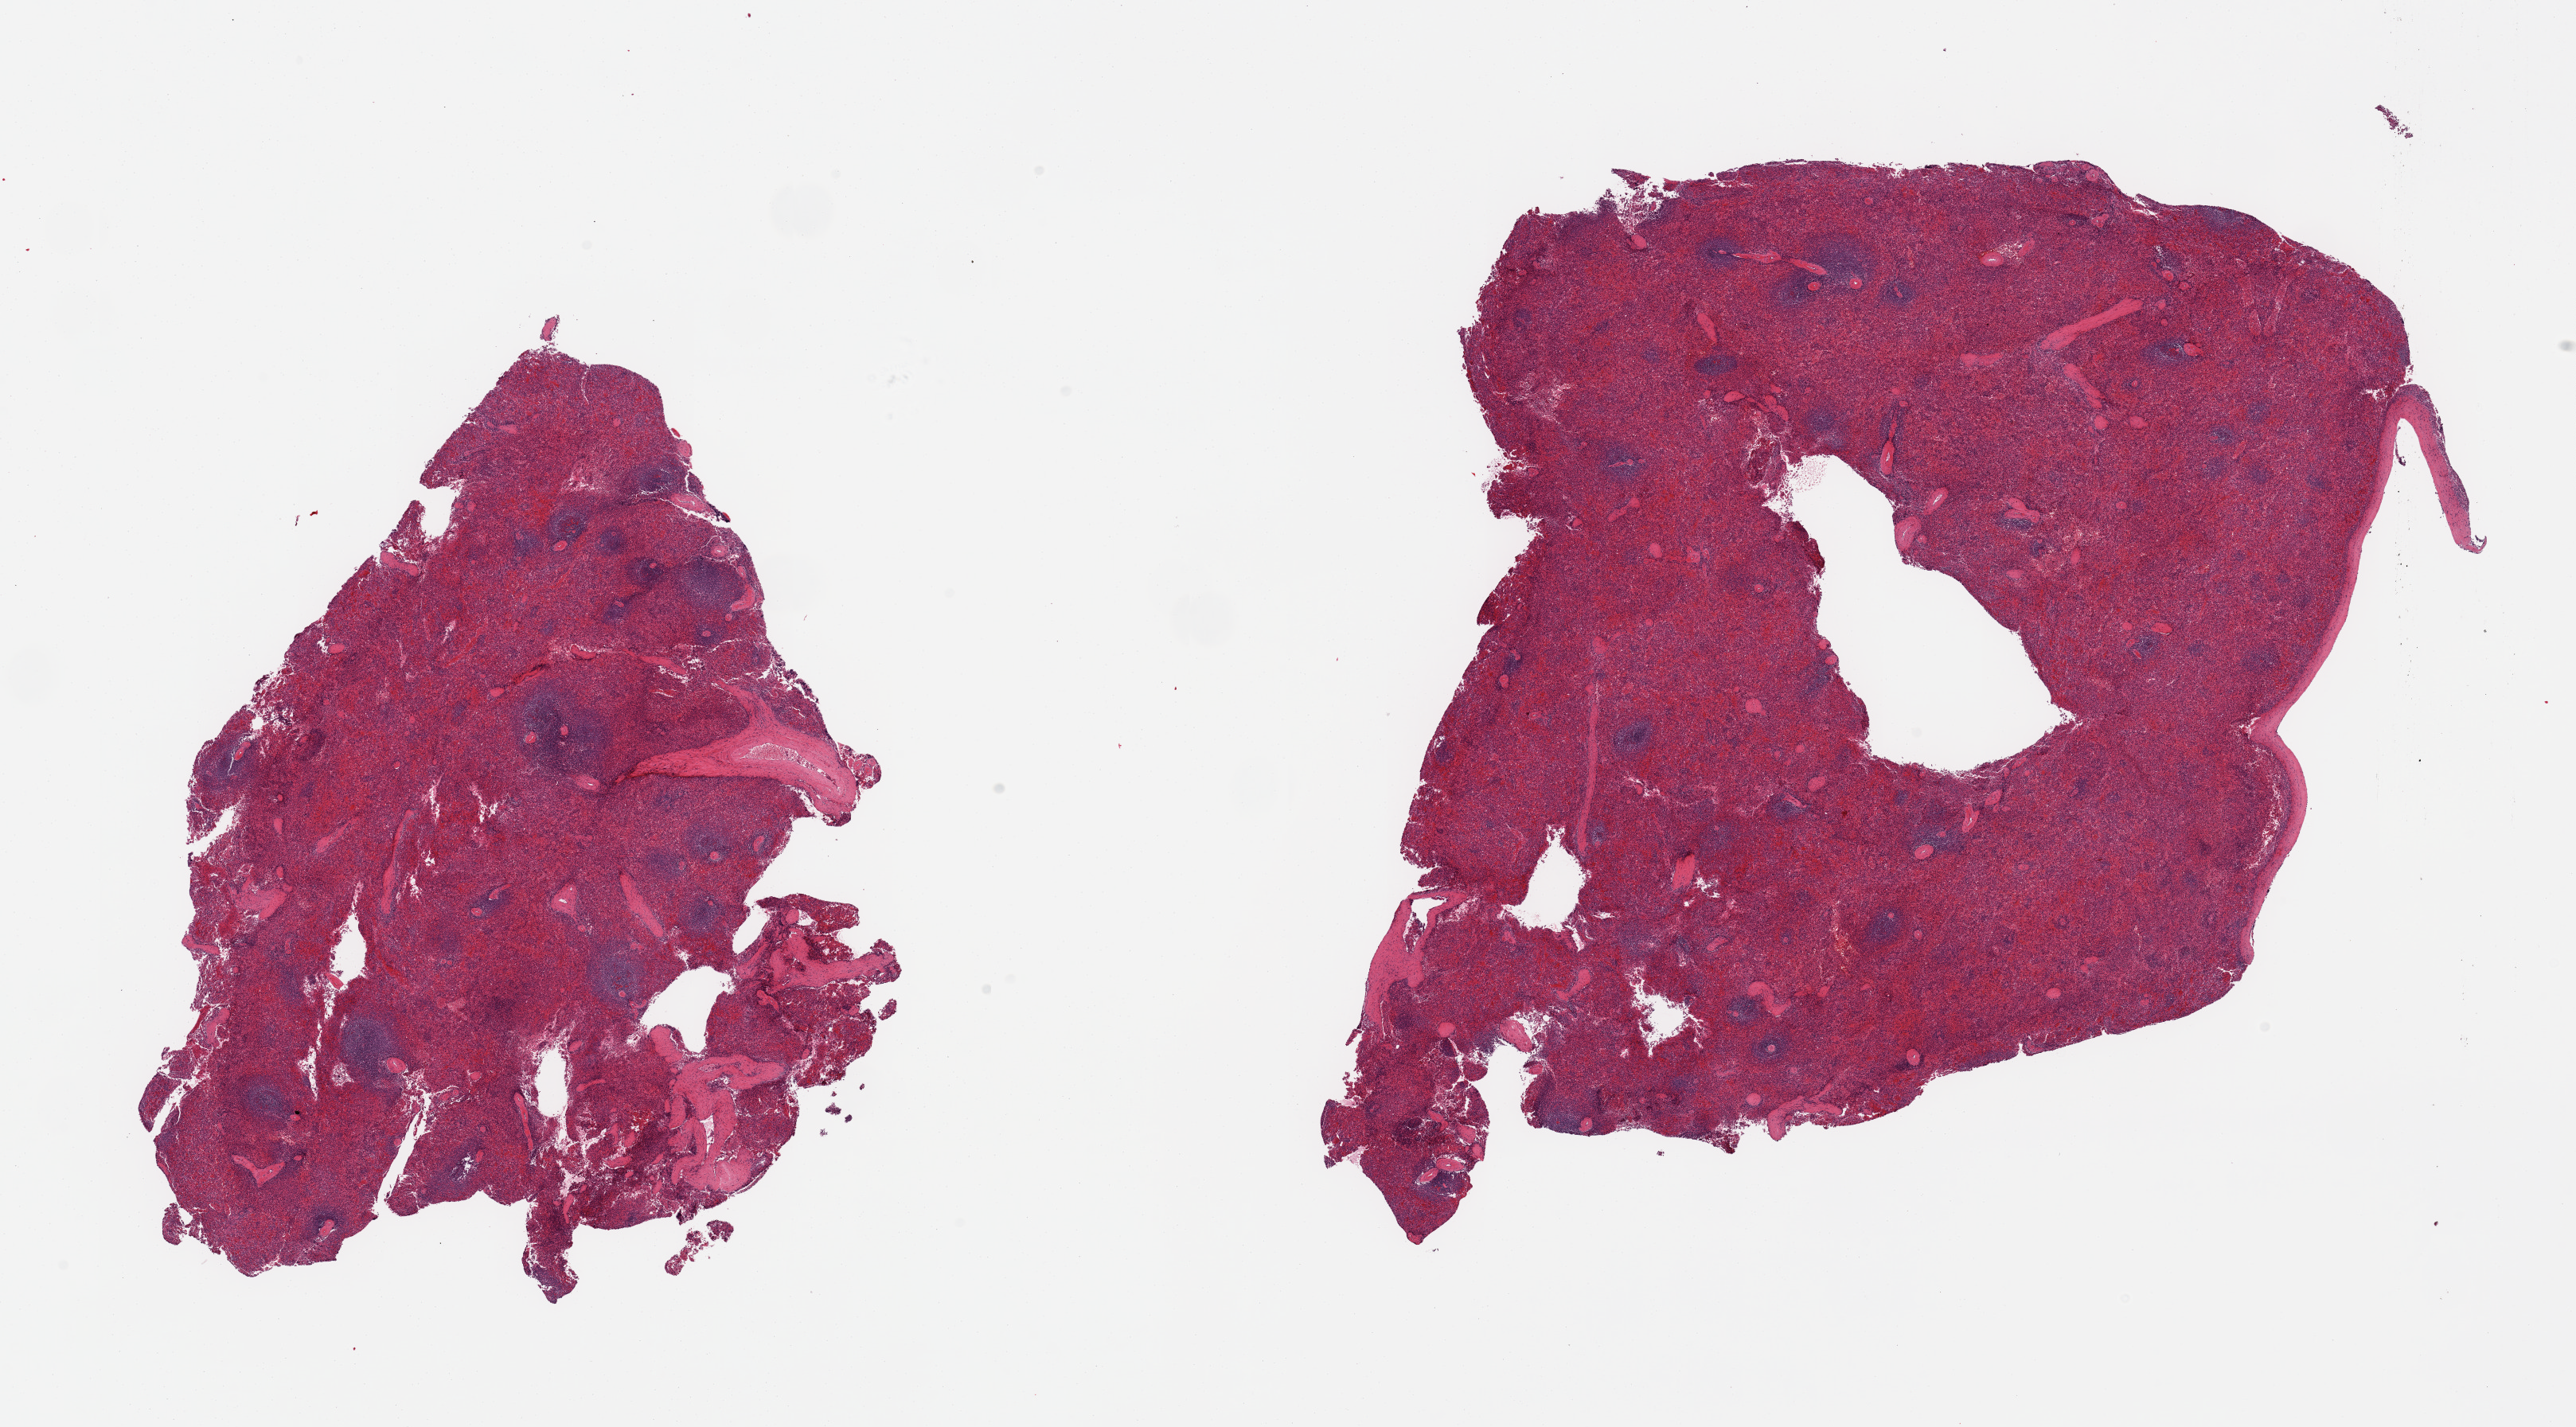
Digitized haematoxylin and eosin-stained section, brightfield — a low-resolution overview of the entire scanned area, about 25.6 x 14.2 mm. PAXgene-fixed paraffin-embedded (PFPE) section. Sampled site (target tissue): spleen. Donor tissue sample. Female donor.
Reviewer comment on this tissue sample: 2 pieces; congested, 1 piece includes capsule (target is 5mm below capsule).